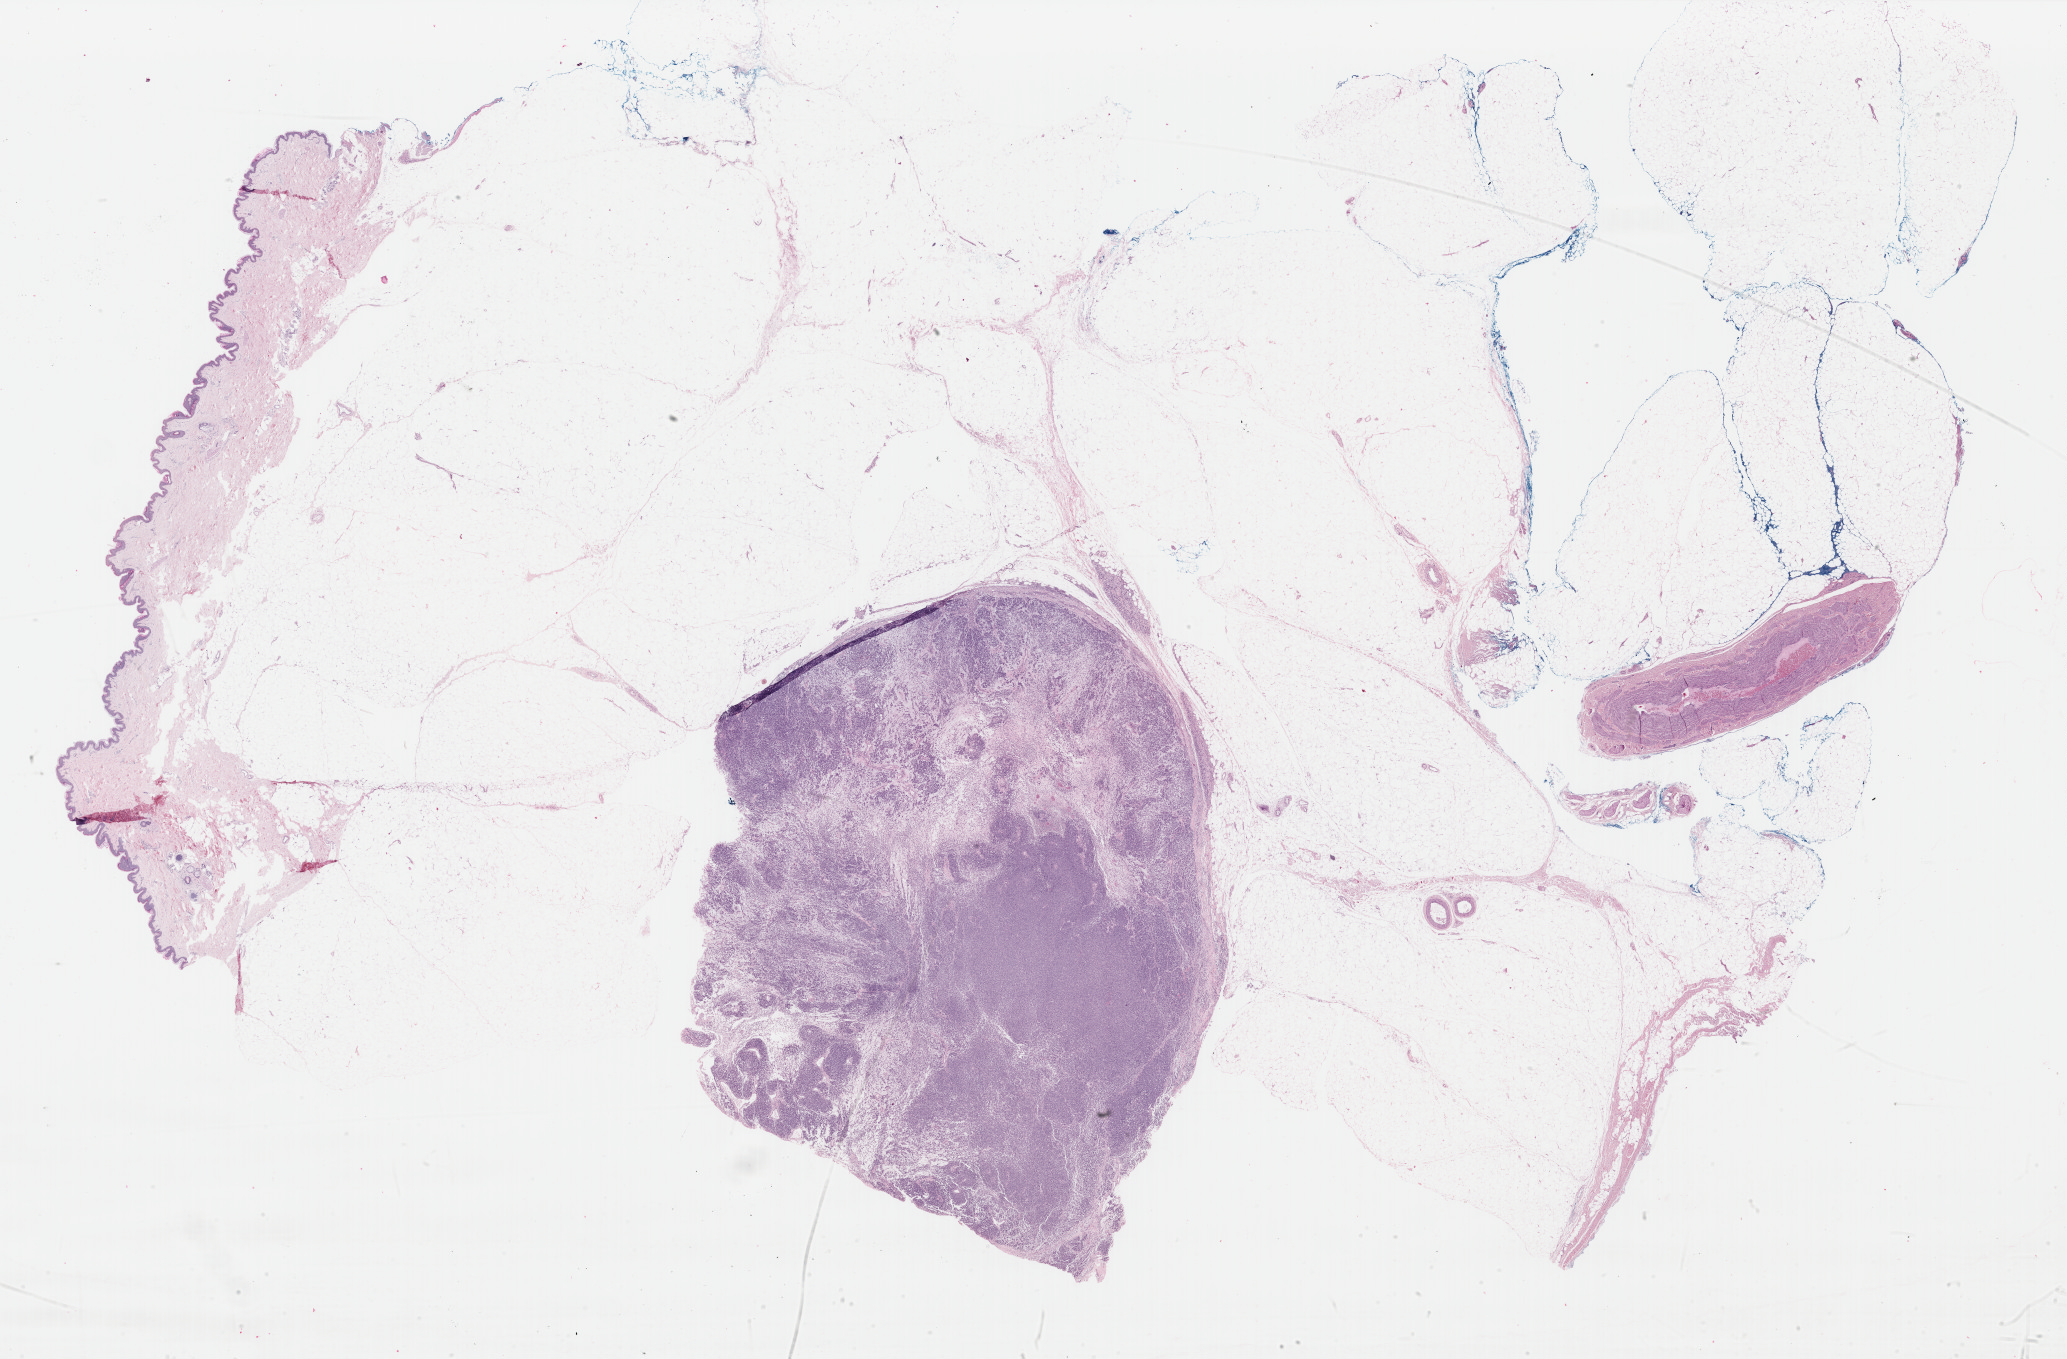
Digitized H&E-stained tissue section (whole slide) — shown as a low-resolution overview of the whole scanned area (about 32.8 x 21.6 mm), formalin-fixed paraffin-embedded (FFPE) diagnostic section, skin, primary tumour sample. Female, age 28 years at initial diagnosis.
Histologic diagnosis: Amelanotic melanoma.